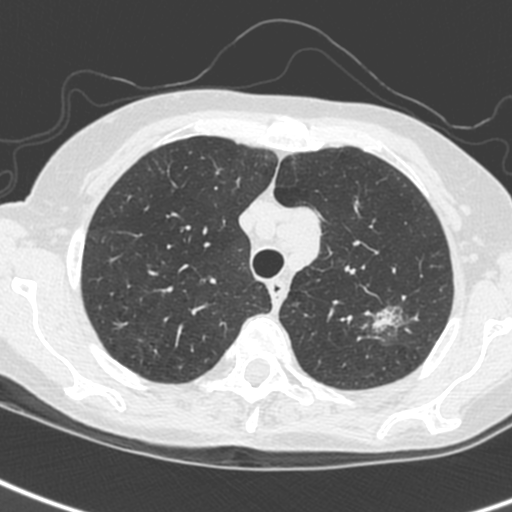
Low-dose screening chest CT, one axial slice. Position 201 of 242 along the scan axis. 120 kVp. Lung window (W 1500 / L -600 HU). 1.3 mm slice thickness. 512 × 512 image matrix.
Outlined on this slice (expert manual segmentation):
- lesion 1 (tumor, upper lobe of left lung): bounding box (x1, y1, x2, y2) in pixels: (373, 308, 399, 330)
- lesion 3 (tumor, upper lobe of left lung): (297, 207, 322, 260)